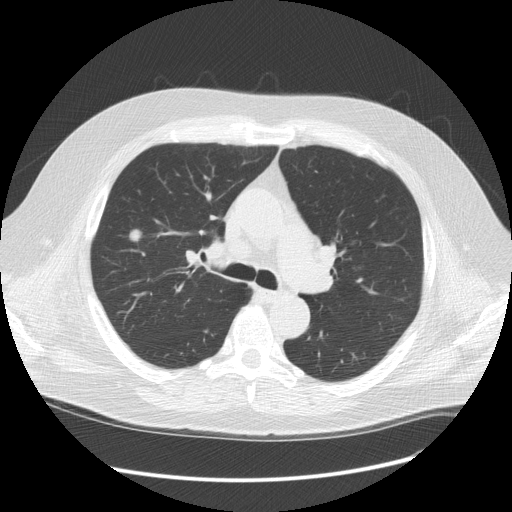
Low-dose screening chest CT, one axial slice; position 84 of 128 along the scan axis; 120 kVp; lung window (W 1500 / L -600 HU); 2.5 mm slice thickness; 512 × 512 image matrix, field of view 401 × 401 mm.
Outlined on this slice (manually delineated by an expert):
- lesion 1 (tumor, upper lobe of right lung): bounding box [x1, y1, x2, y2] px = [130, 230, 140, 241]